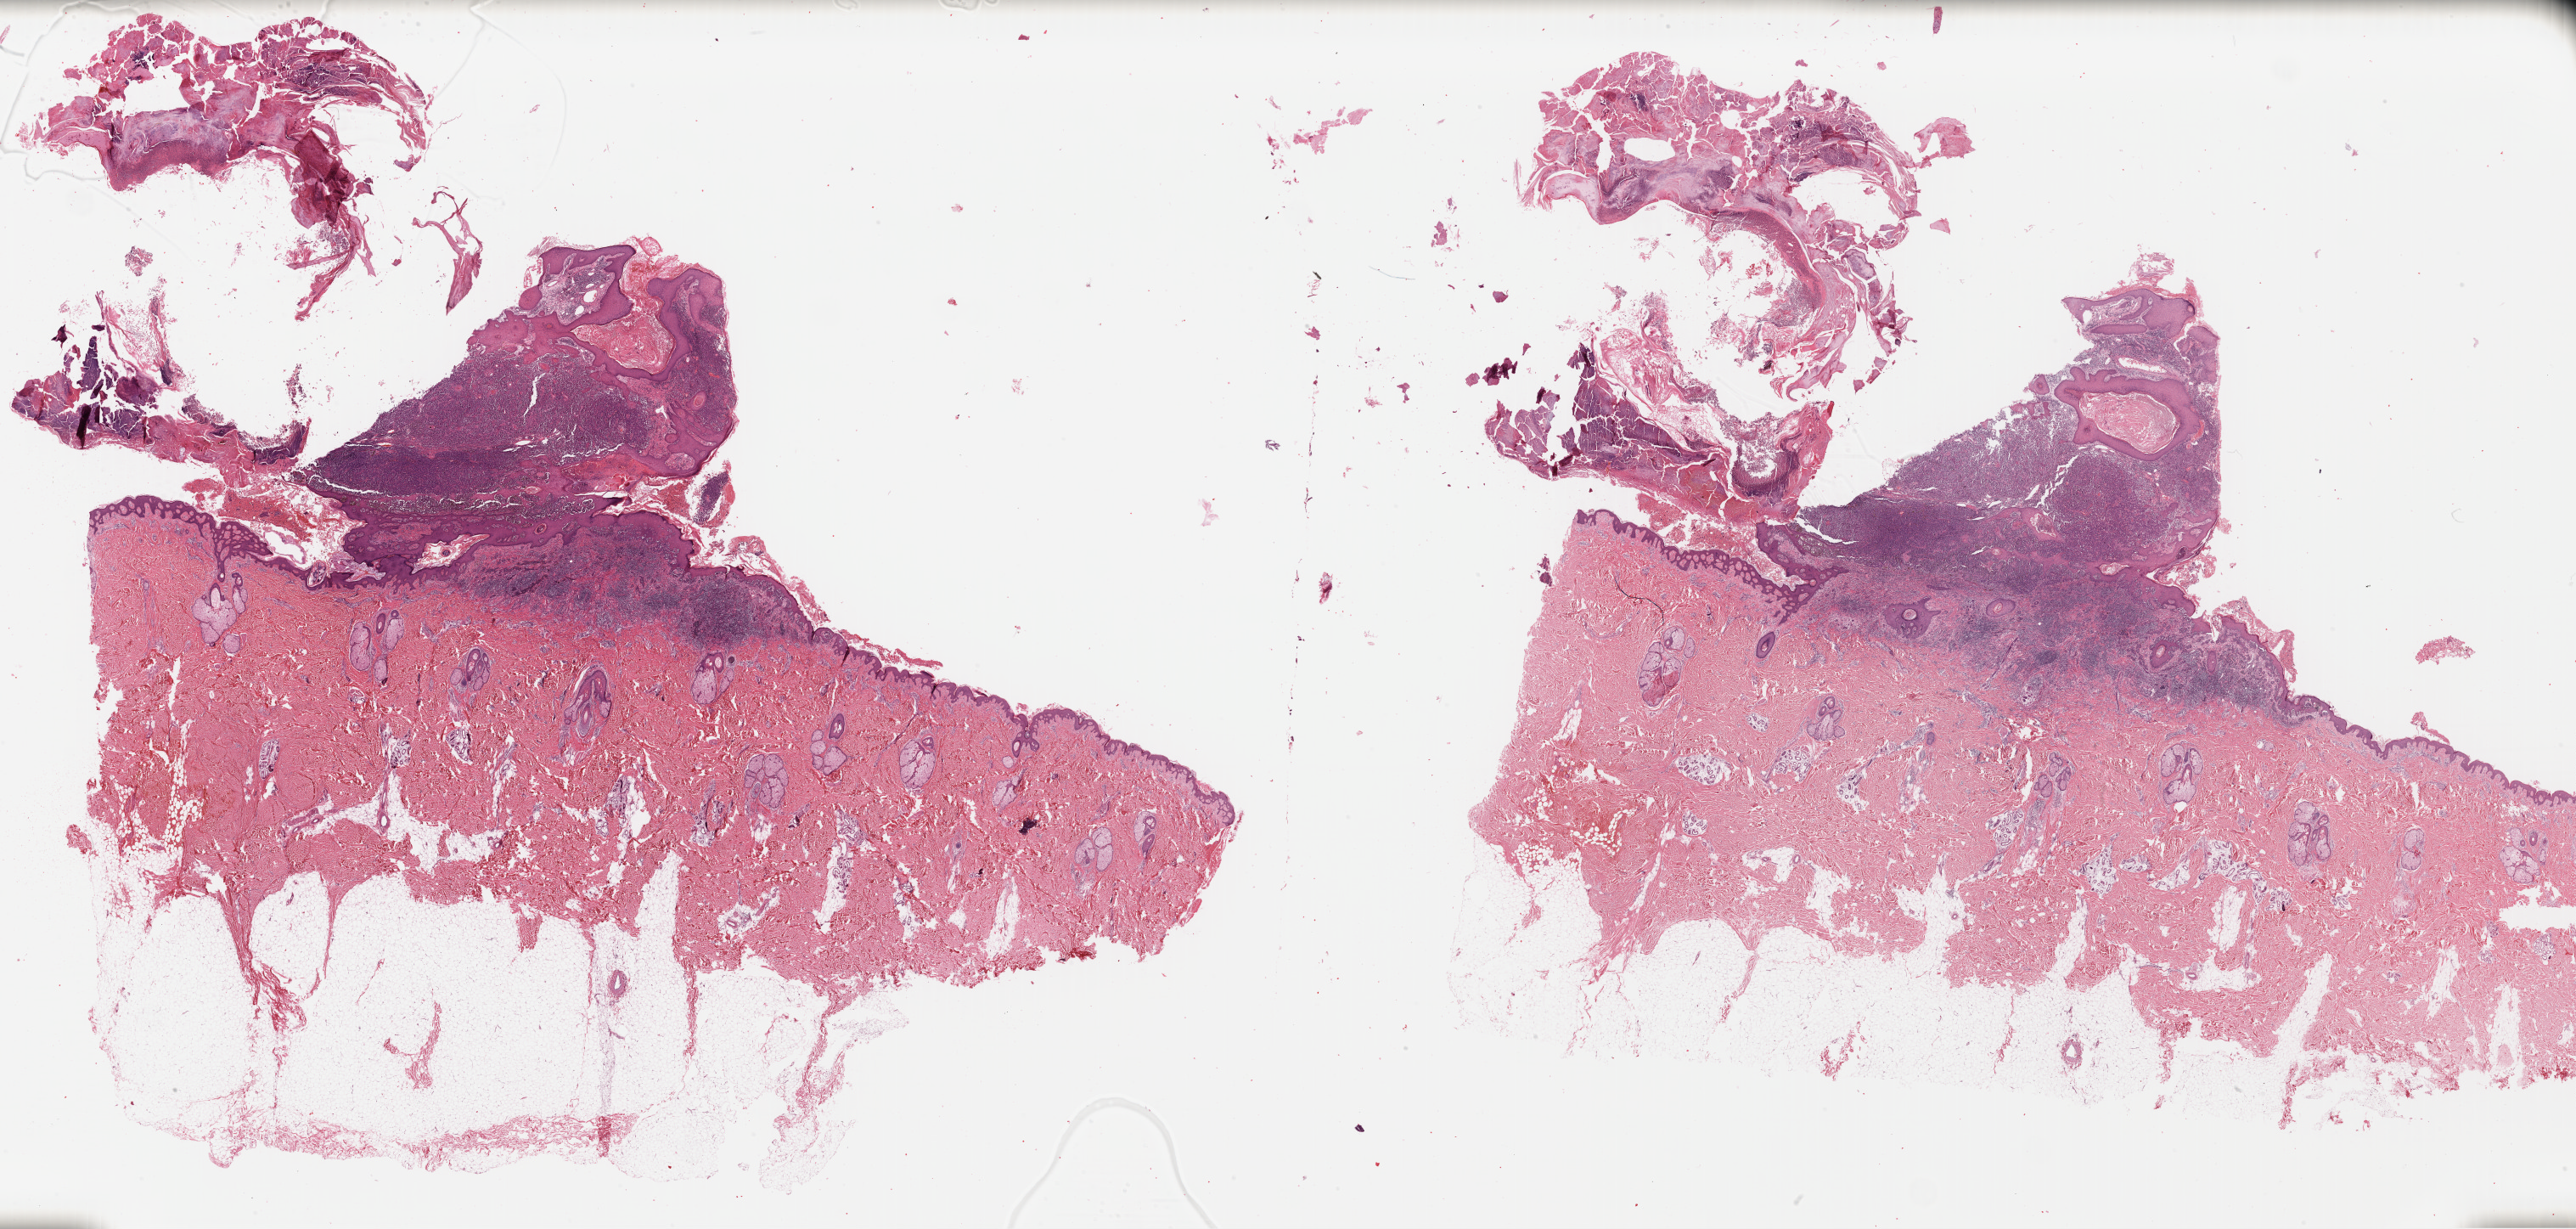
Digitized H&E-stained tissue section (whole slide) — shown as a low-resolution overview of the whole scanned area (about 47.7 x 22.7 mm). Formalin-fixed paraffin-embedded (FFPE) diagnostic section. Sample: primary tumour, skin. Male, age 43 years at initial diagnosis.
- AJCC pathologic stage: IIIA (5th edition)
- diagnosis: Malignant melanoma, NOS